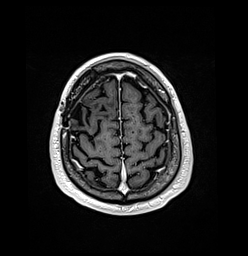
Brain MRI from a brain-tumour surgery series, one axial slice; position 31 of 176 along the scan axis; T1-weighted post-contrast; 248 × 256 image matrix, field of view 242 × 250 mm. Case-level facts recorded for this patient, not image findings: histopathology: Oligodendroglioma; WHO grade: 3; IDH mutation: yes; tumour location: Right Frontal.
Structures marked on this image (expert manual segmentation):
- previous resection cavity: box from (x=71, y=102) to (x=84, y=126) px